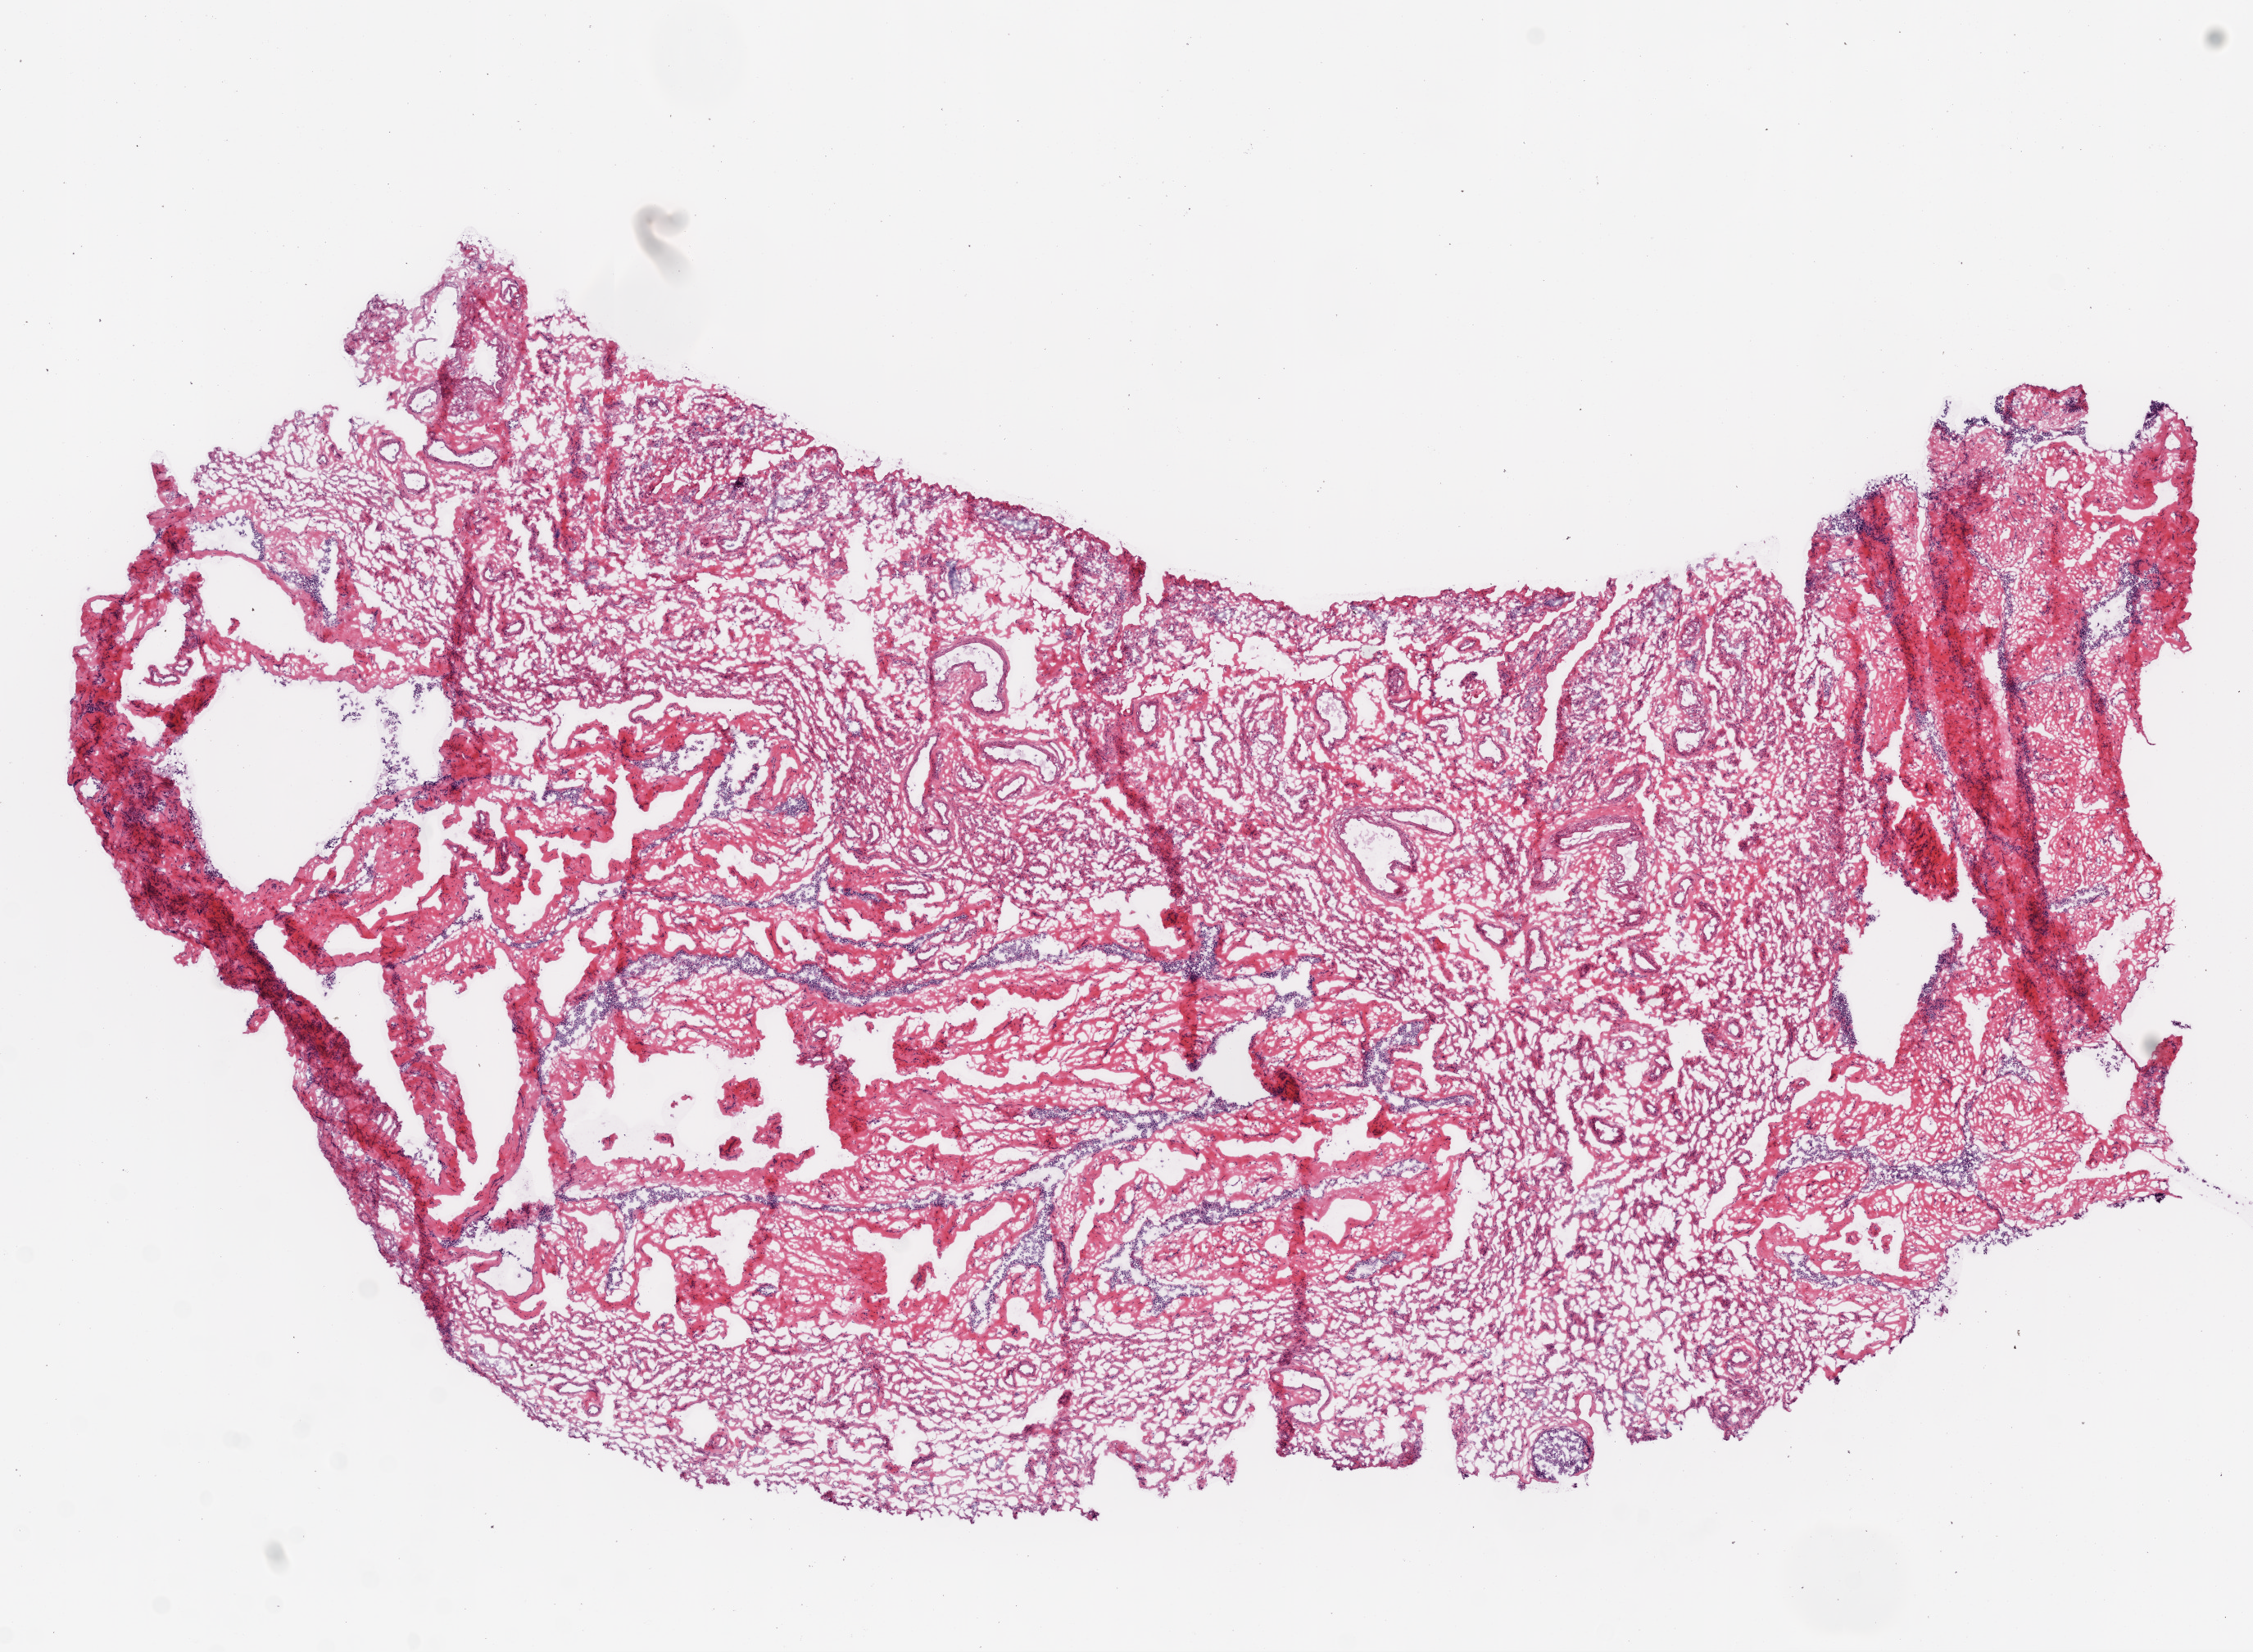
H&E whole-slide image, whole scanned area (about 11.0 x 8.1 mm, from a 20x scan) shown as a low-resolution overview. Frozen section from the top of the tissue portion. Ovary, solid tissue normal (non-tumour tissue) sample. Patient: female, age at initial diagnosis 74 years.
This section: solid tissue normal sample (biorepository sample class). Patient diagnosis: Serous cystadenocarcinoma, NOS.